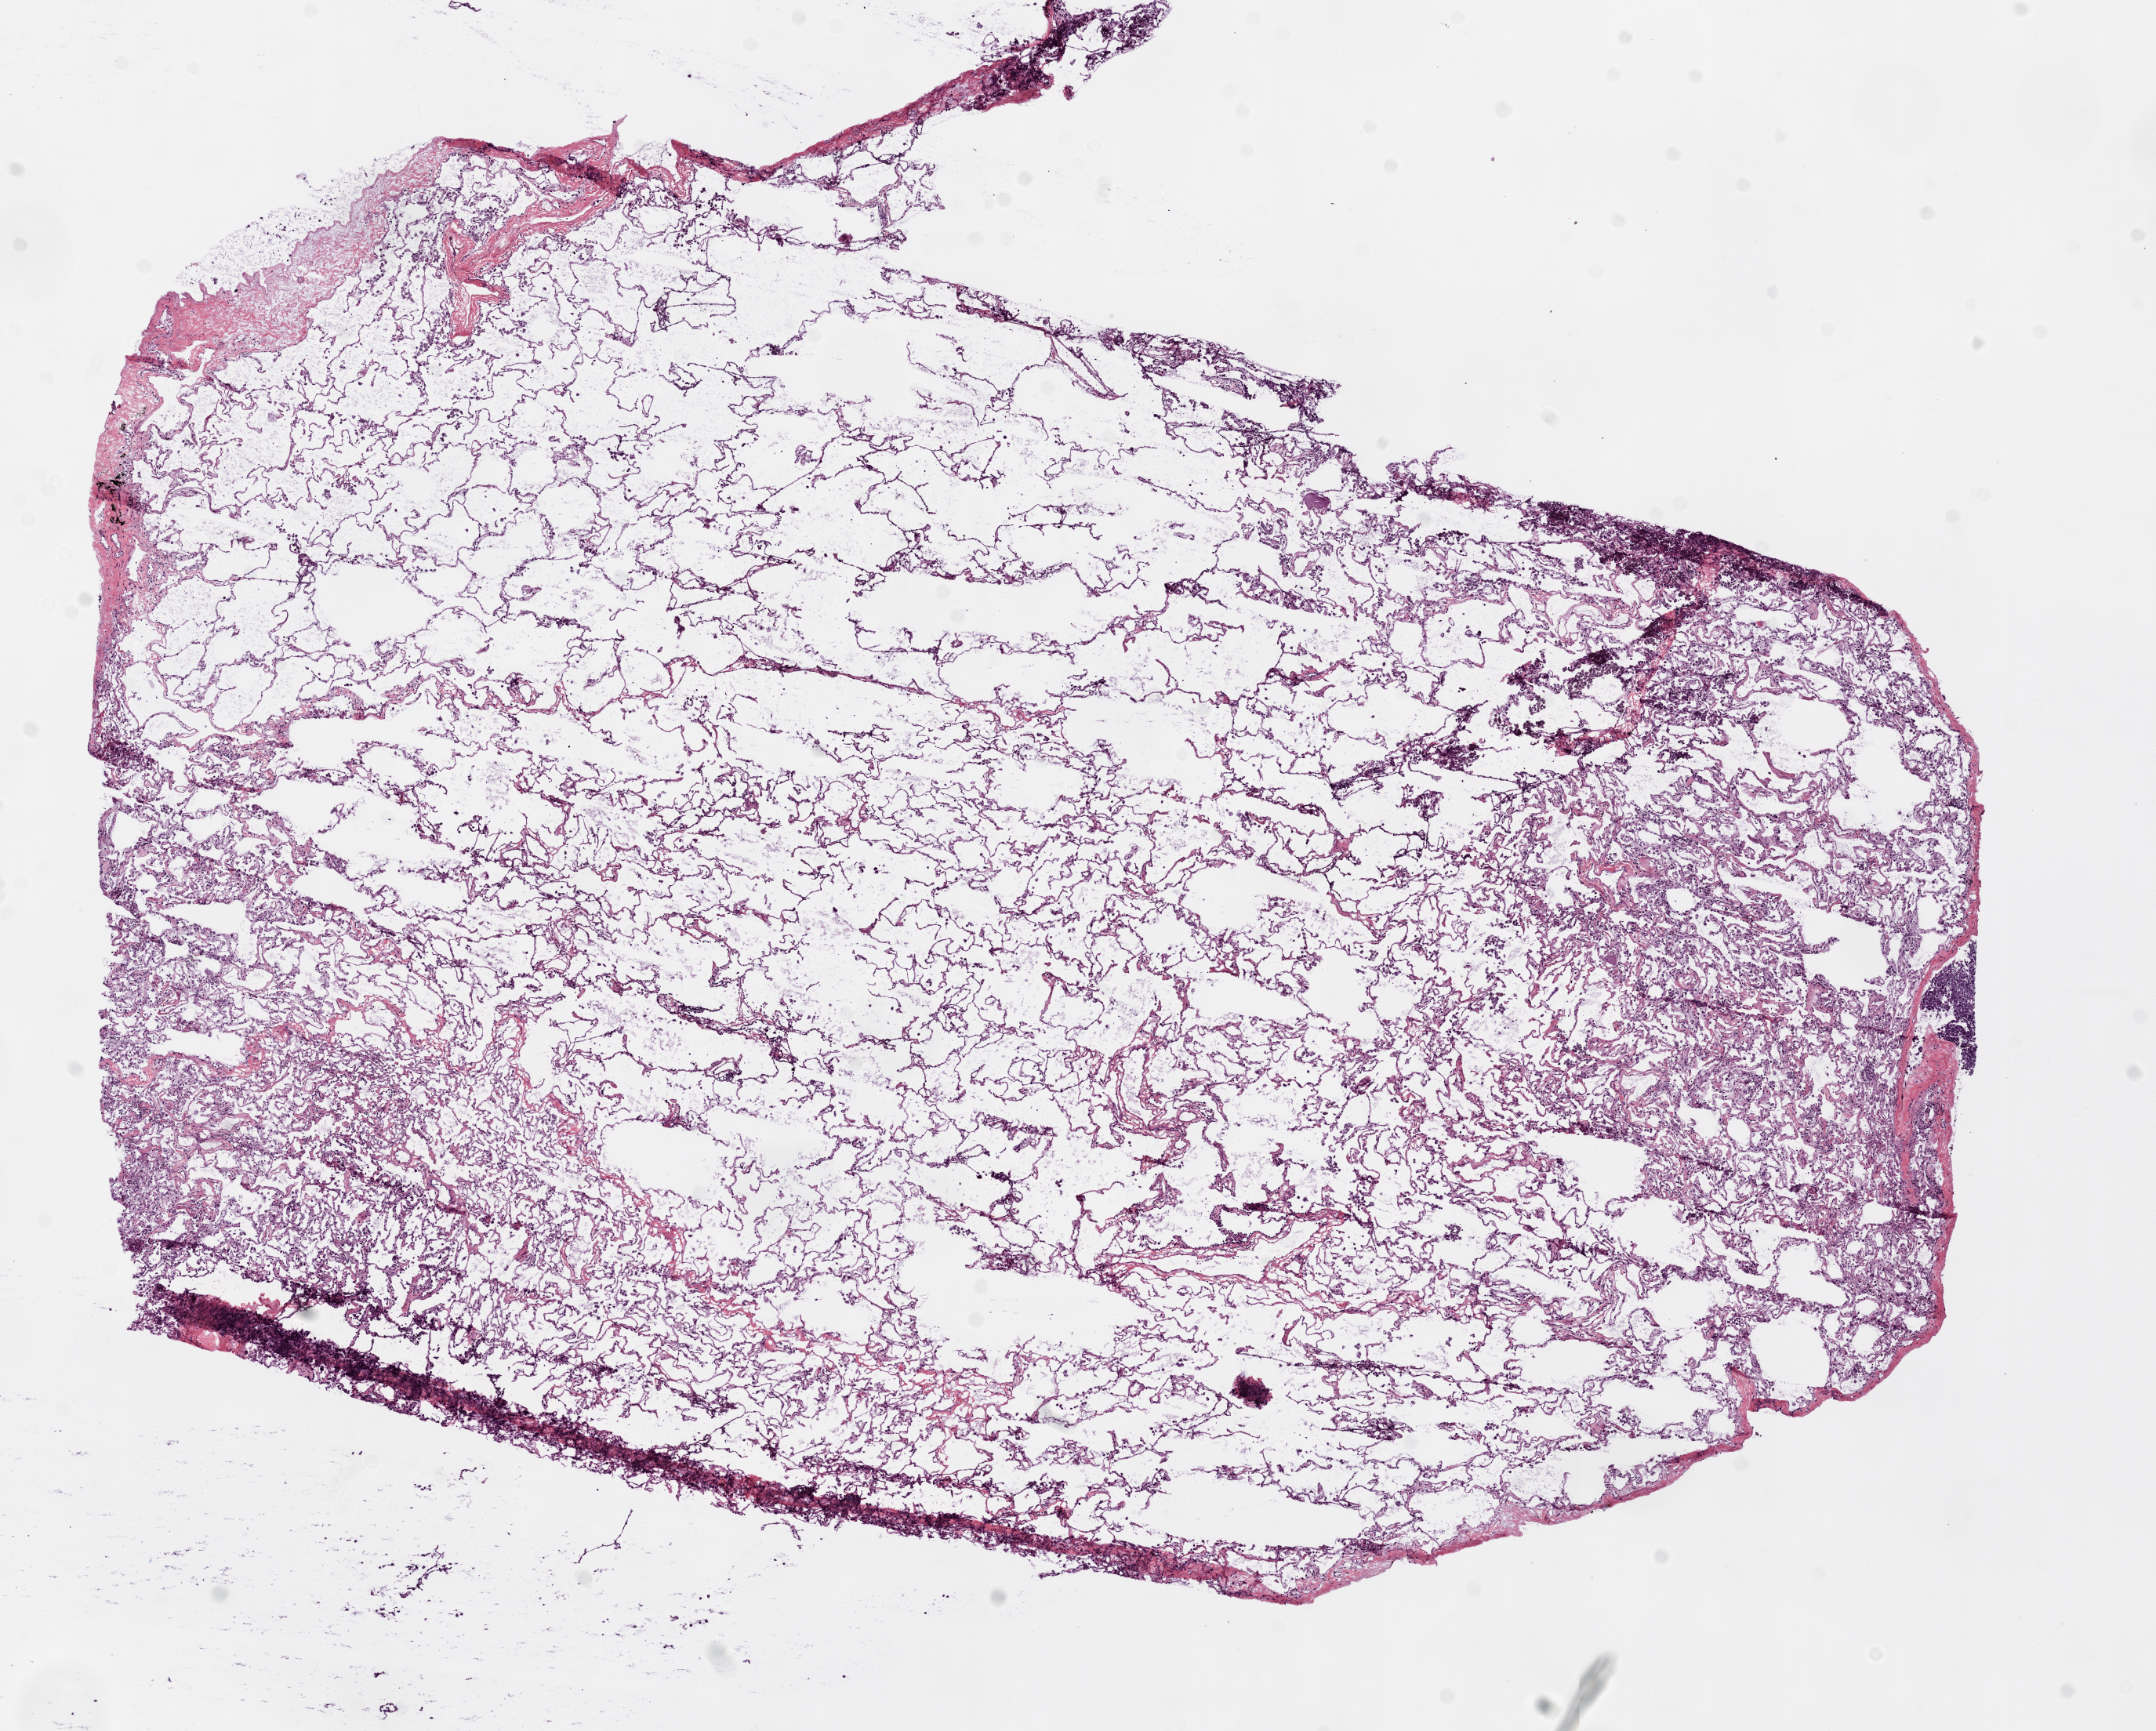
Hematoxylin and eosin (H&E) stained whole-slide image — low-resolution overview of the scanned area, about 11.0 x 8.9 mm; frozen section; lung, solid tissue normal (non-tumour tissue) sample. Female patient; age at initial diagnosis 52 years.
This section: solid tissue normal (non-tumour) sample from the same patient. Patient diagnosis: Adenocarcinoma, NOS.